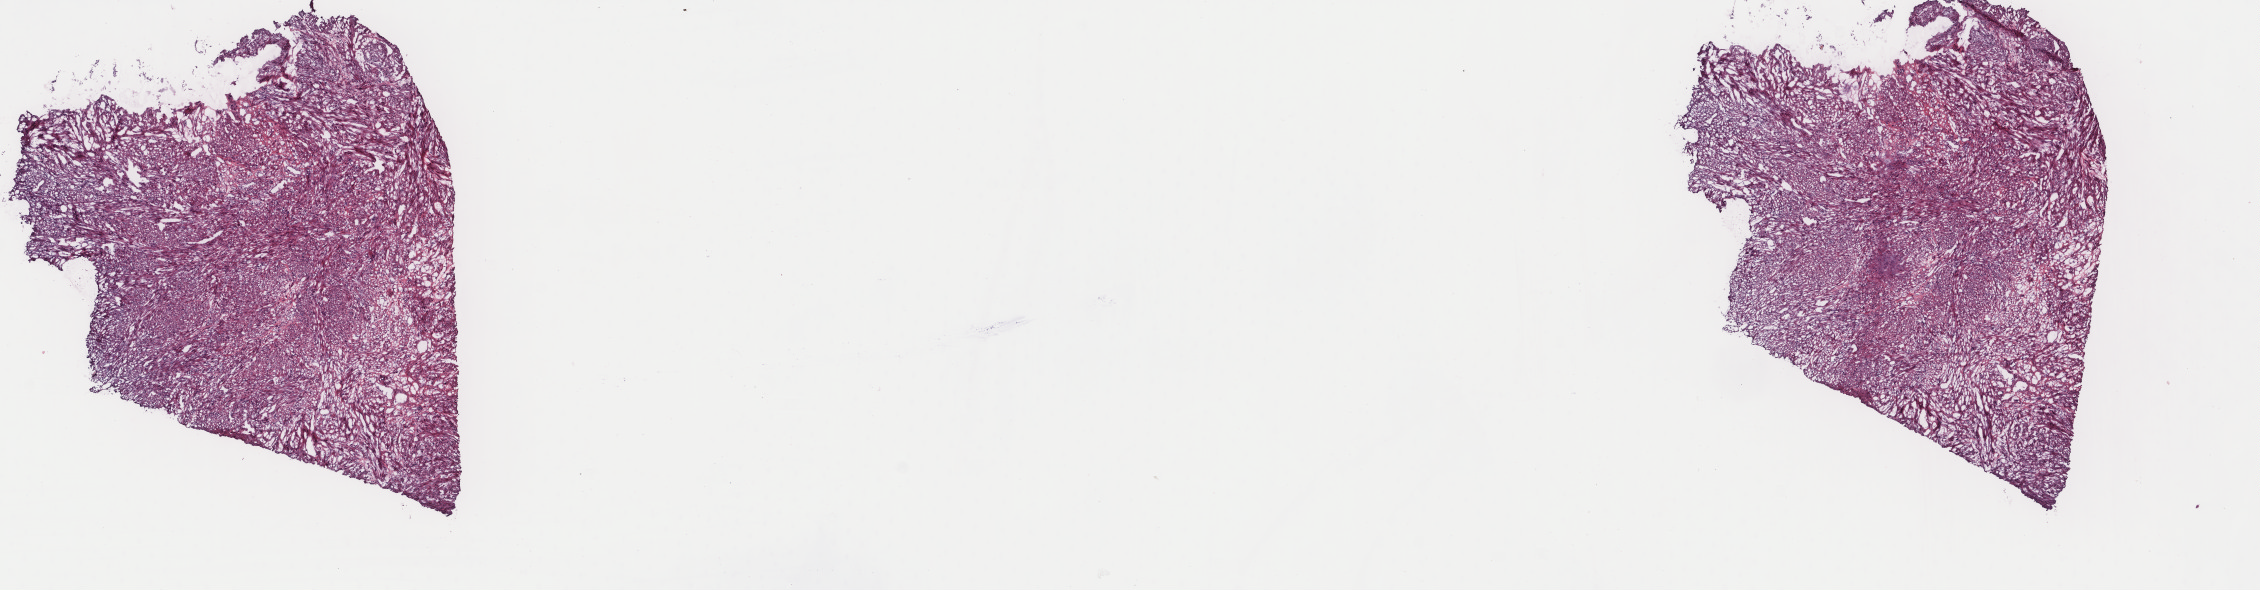
H&E-stained whole-slide image, shown as a low-resolution overview of the whole scanned area (about 17.9 x 4.7 mm), frozen section, sample: primary tumour, retroperitoneum and peritoneum. Female patient; age at initial diagnosis 54 years. Slide review estimates, as recorded: tumour cells 75%, tumour nuclei 75%, normal cells 4%, stromal cells 21%, necrosis 0%. Inflammatory infiltration, as recorded: lymphocyte infiltration 1%, monocyte infiltration 1%, neutrophil infiltration 0%.
Histologic diagnosis: Leiomyosarcoma, NOS (retroperitoneum).